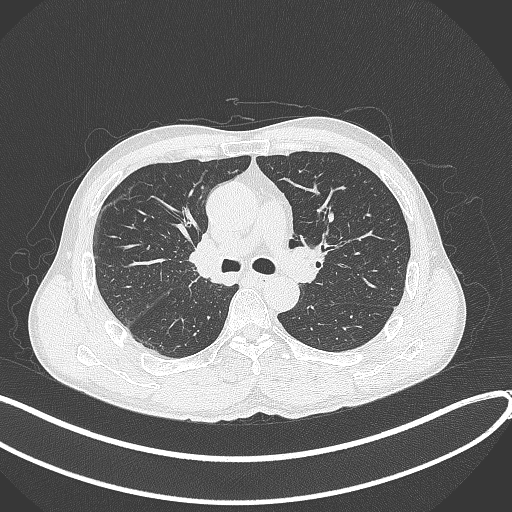
Chest CT, one axial slice; slice 239 of 409 in the series (ordered by position); reconstruction kernel B70f; 120 kVp; lung window (W 1500 / L -600 HU); 1 mm slice thickness; 512 × 512 image matrix, field of view 400 × 400 mm. Male patient, age 53 years. Case-level facts recorded for this patient, not image findings: clinical TNM (as recorded): T1b N0 M0.
Structures marked on this image (bounding box drawn by a radiologist):
- lung tumour (recorded histology: squamous cell carcinoma): bounding box <184,234,229,292> (left, top, right, bottom; pixels)